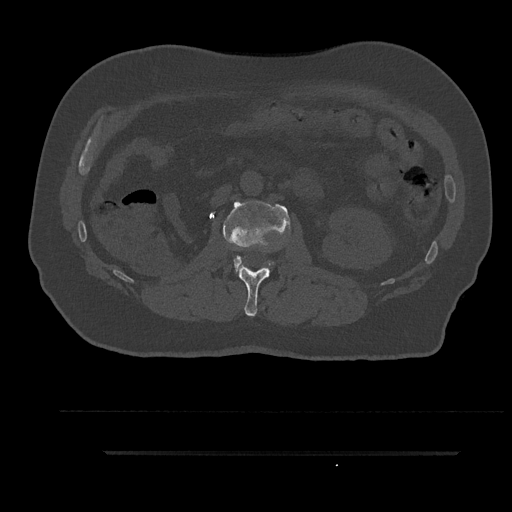
CT including the spine, one axial slice; position 143 of 797 along the scan axis; bone window (W 1800 / L 400 HU); 0.5 mm slice thickness; 512 × 512 image matrix, field of view 432 × 432 mm. Patient: male, 63 years. From the clinical record (not read from this slice): primary cancer: renal; vertebrae with lytic lesions (as recorded): T8.
Structures marked on this image (semi-automatically segmented with operator editing):
- L1 vertebra: bounding box (x1, y1, x2, y2) in pixels: (237, 265, 270, 316)
- L2 vertebra: (223, 201, 290, 271)